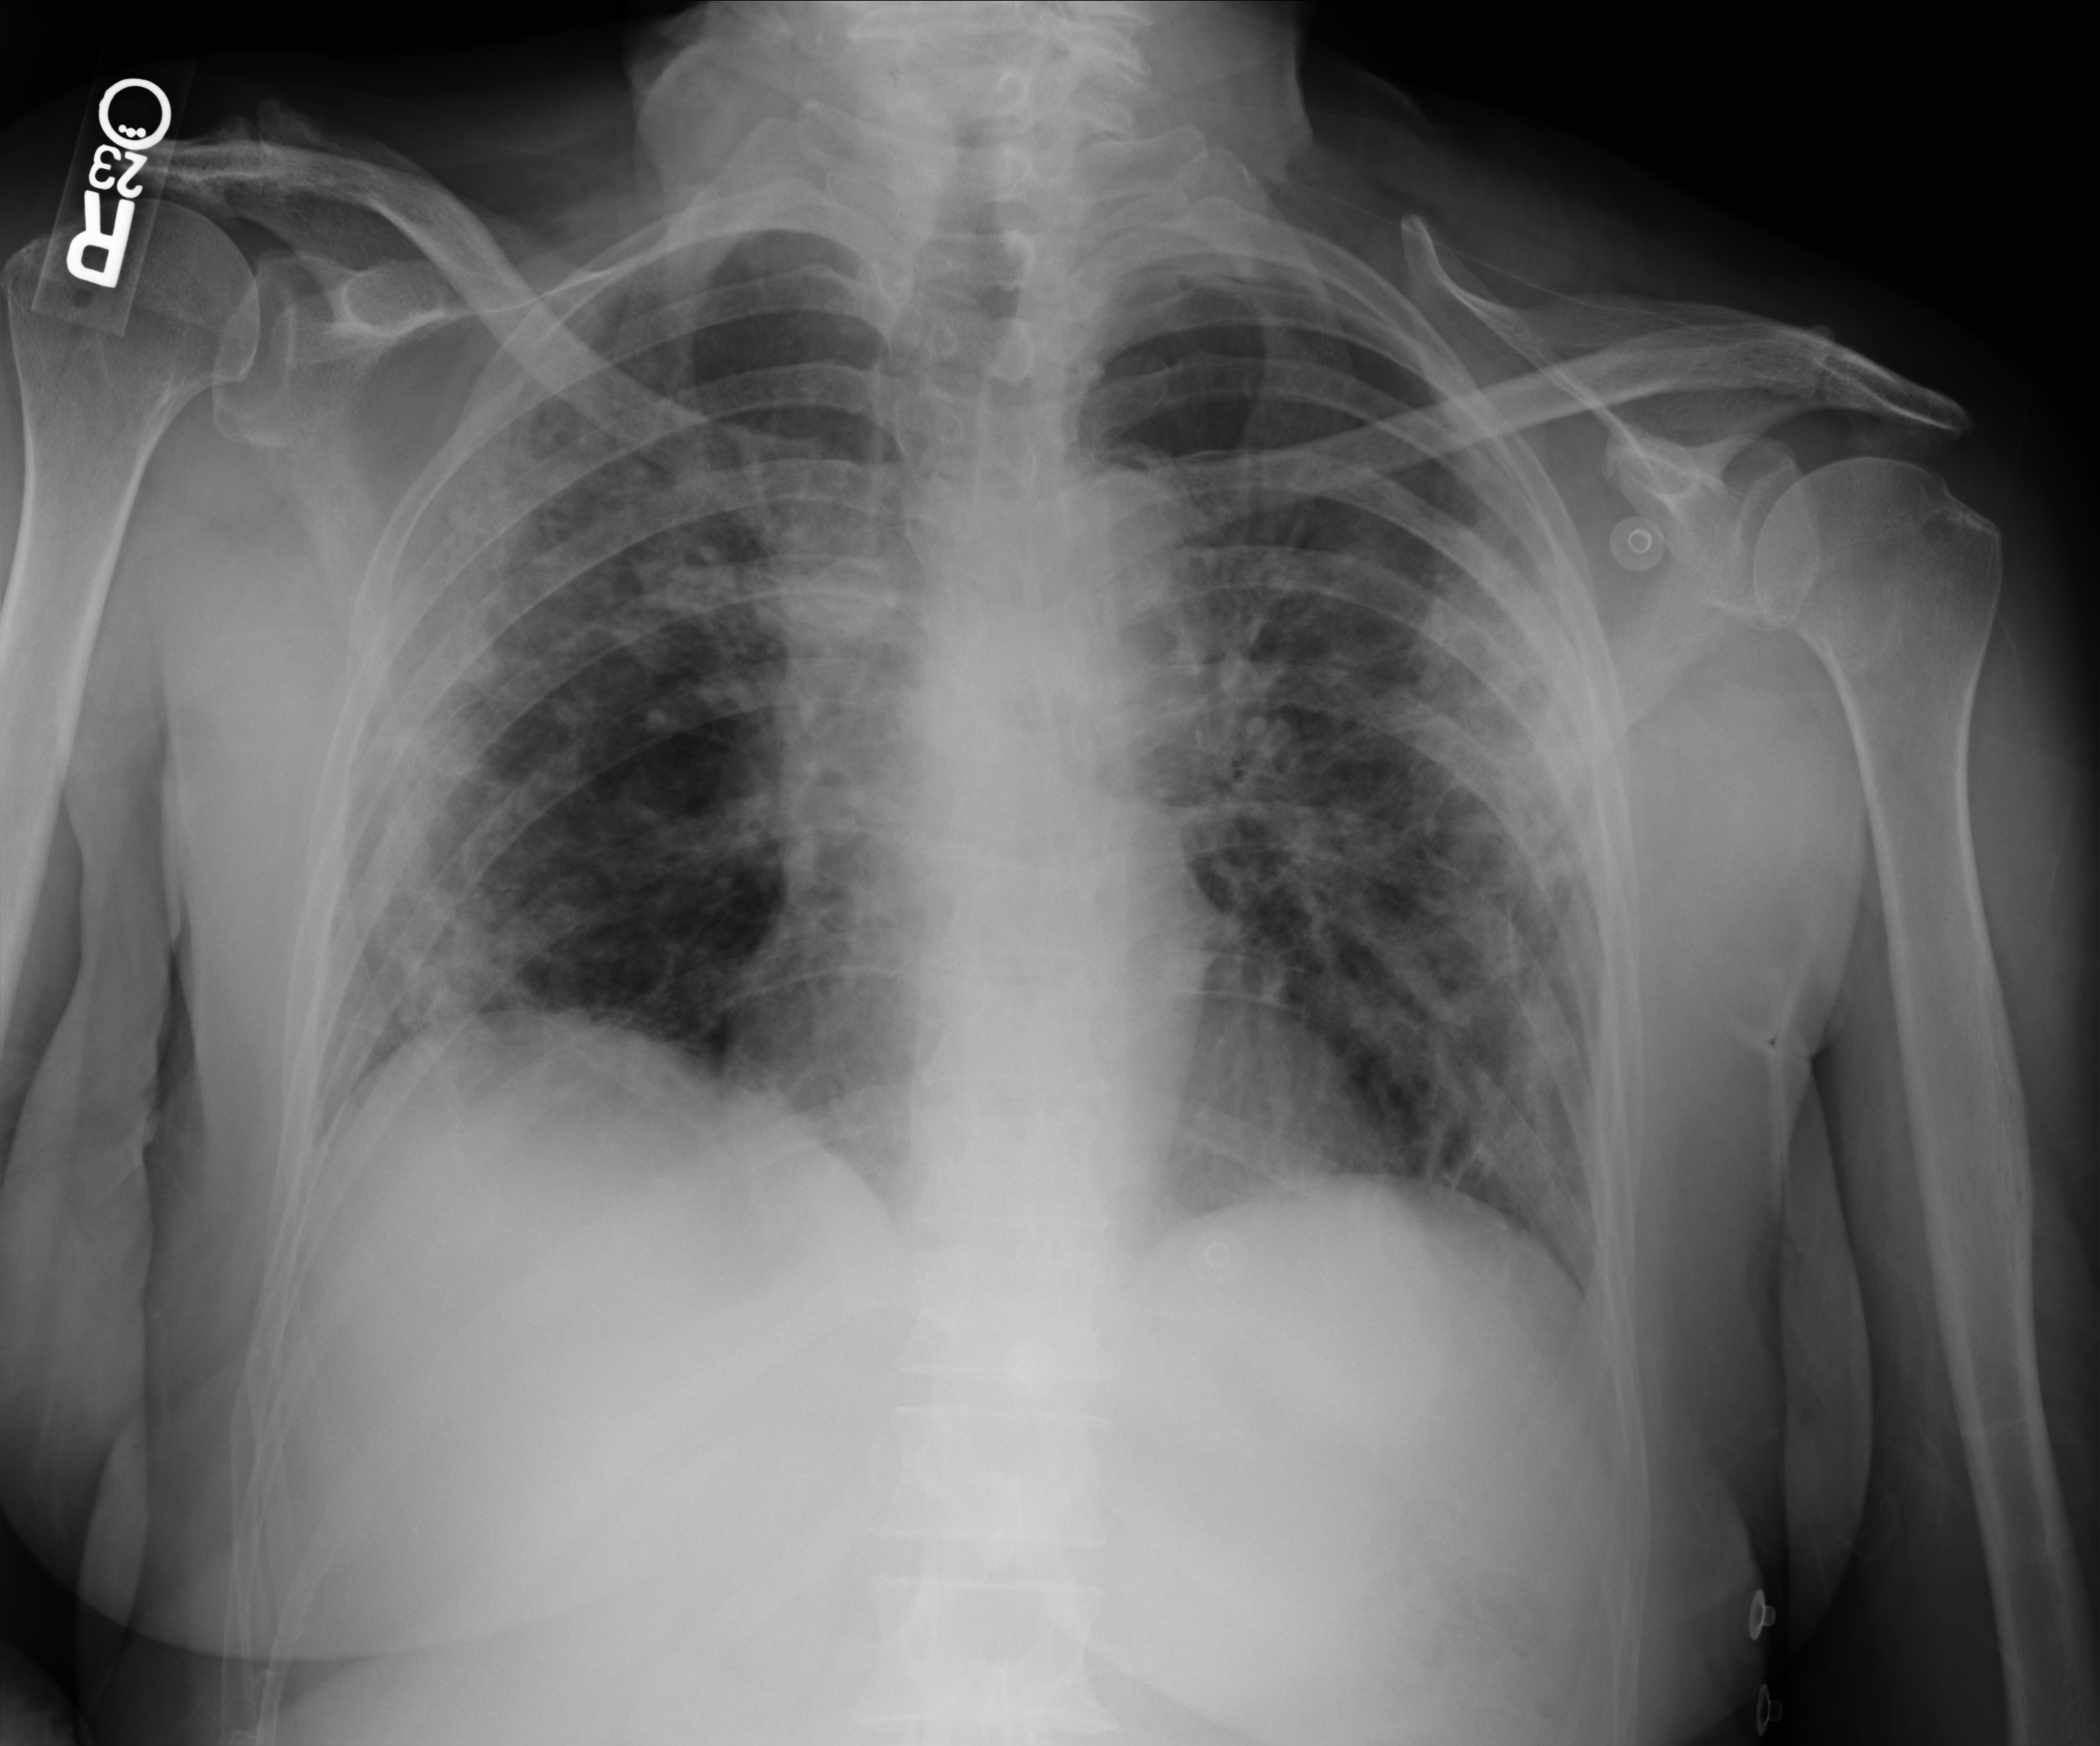
Chest X-ray (portable); anteroposterior (AP) projection. Female patient hospitalised with COVID-19, age 60–74 years.
From the hospital-stay record, not from the radiograph (when in the stay this image was taken is not recorded):
- chronic kidney disease (admission record): no
- mechanically ventilated during this hospital stay: yes
- admitted to intensive care during this hospital stay: yes